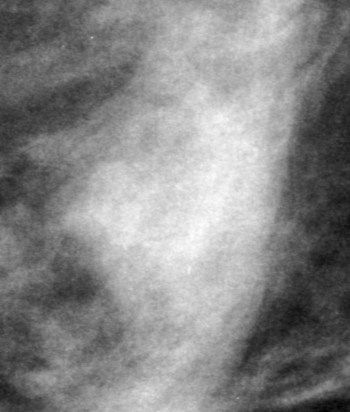
Cropped region of a digitized screen-film mammogram centred on a radiologist-marked abnormality, right breast, MLO view.
- Finding: mass, shape oval, margins obscured; BI-RADS assessment category 0 (incomplete: needs additional imaging); pathology result (as recorded, not read from the image): benign.